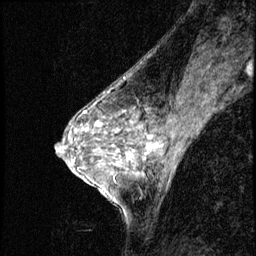
Breast MRI (dynamic contrast-enhanced), one sagittal slice; slice 31 of 56 in the series (ordered by position); dynamic contrast-enhanced series, image 2 of 3 at this slice position (ordered by acquisition); 1.5 T; TE 4.2 ms, TR 8.7 ms; 2.5 mm slice thickness; 256 × 256 image matrix. Patient: female, 50 years. Case-level facts recorded for this patient, not image findings: setting: breast cancer imaged before/during neoadjuvant chemotherapy; receptor status: HR-positive, HER2-negative.
Annotated regions visible in this slice (semi-automatically segmented with operator editing):
- analysis volume of interest (the breast-tissue region the enhancement analysis was run in; not a lesion): box from (x=119, y=136) to (x=169, y=190) px
- tumour enhancement mask (voxels above the 140 % enhancement threshold inside the analysis volume of interest): (x=128, y=144)–(x=155, y=156)